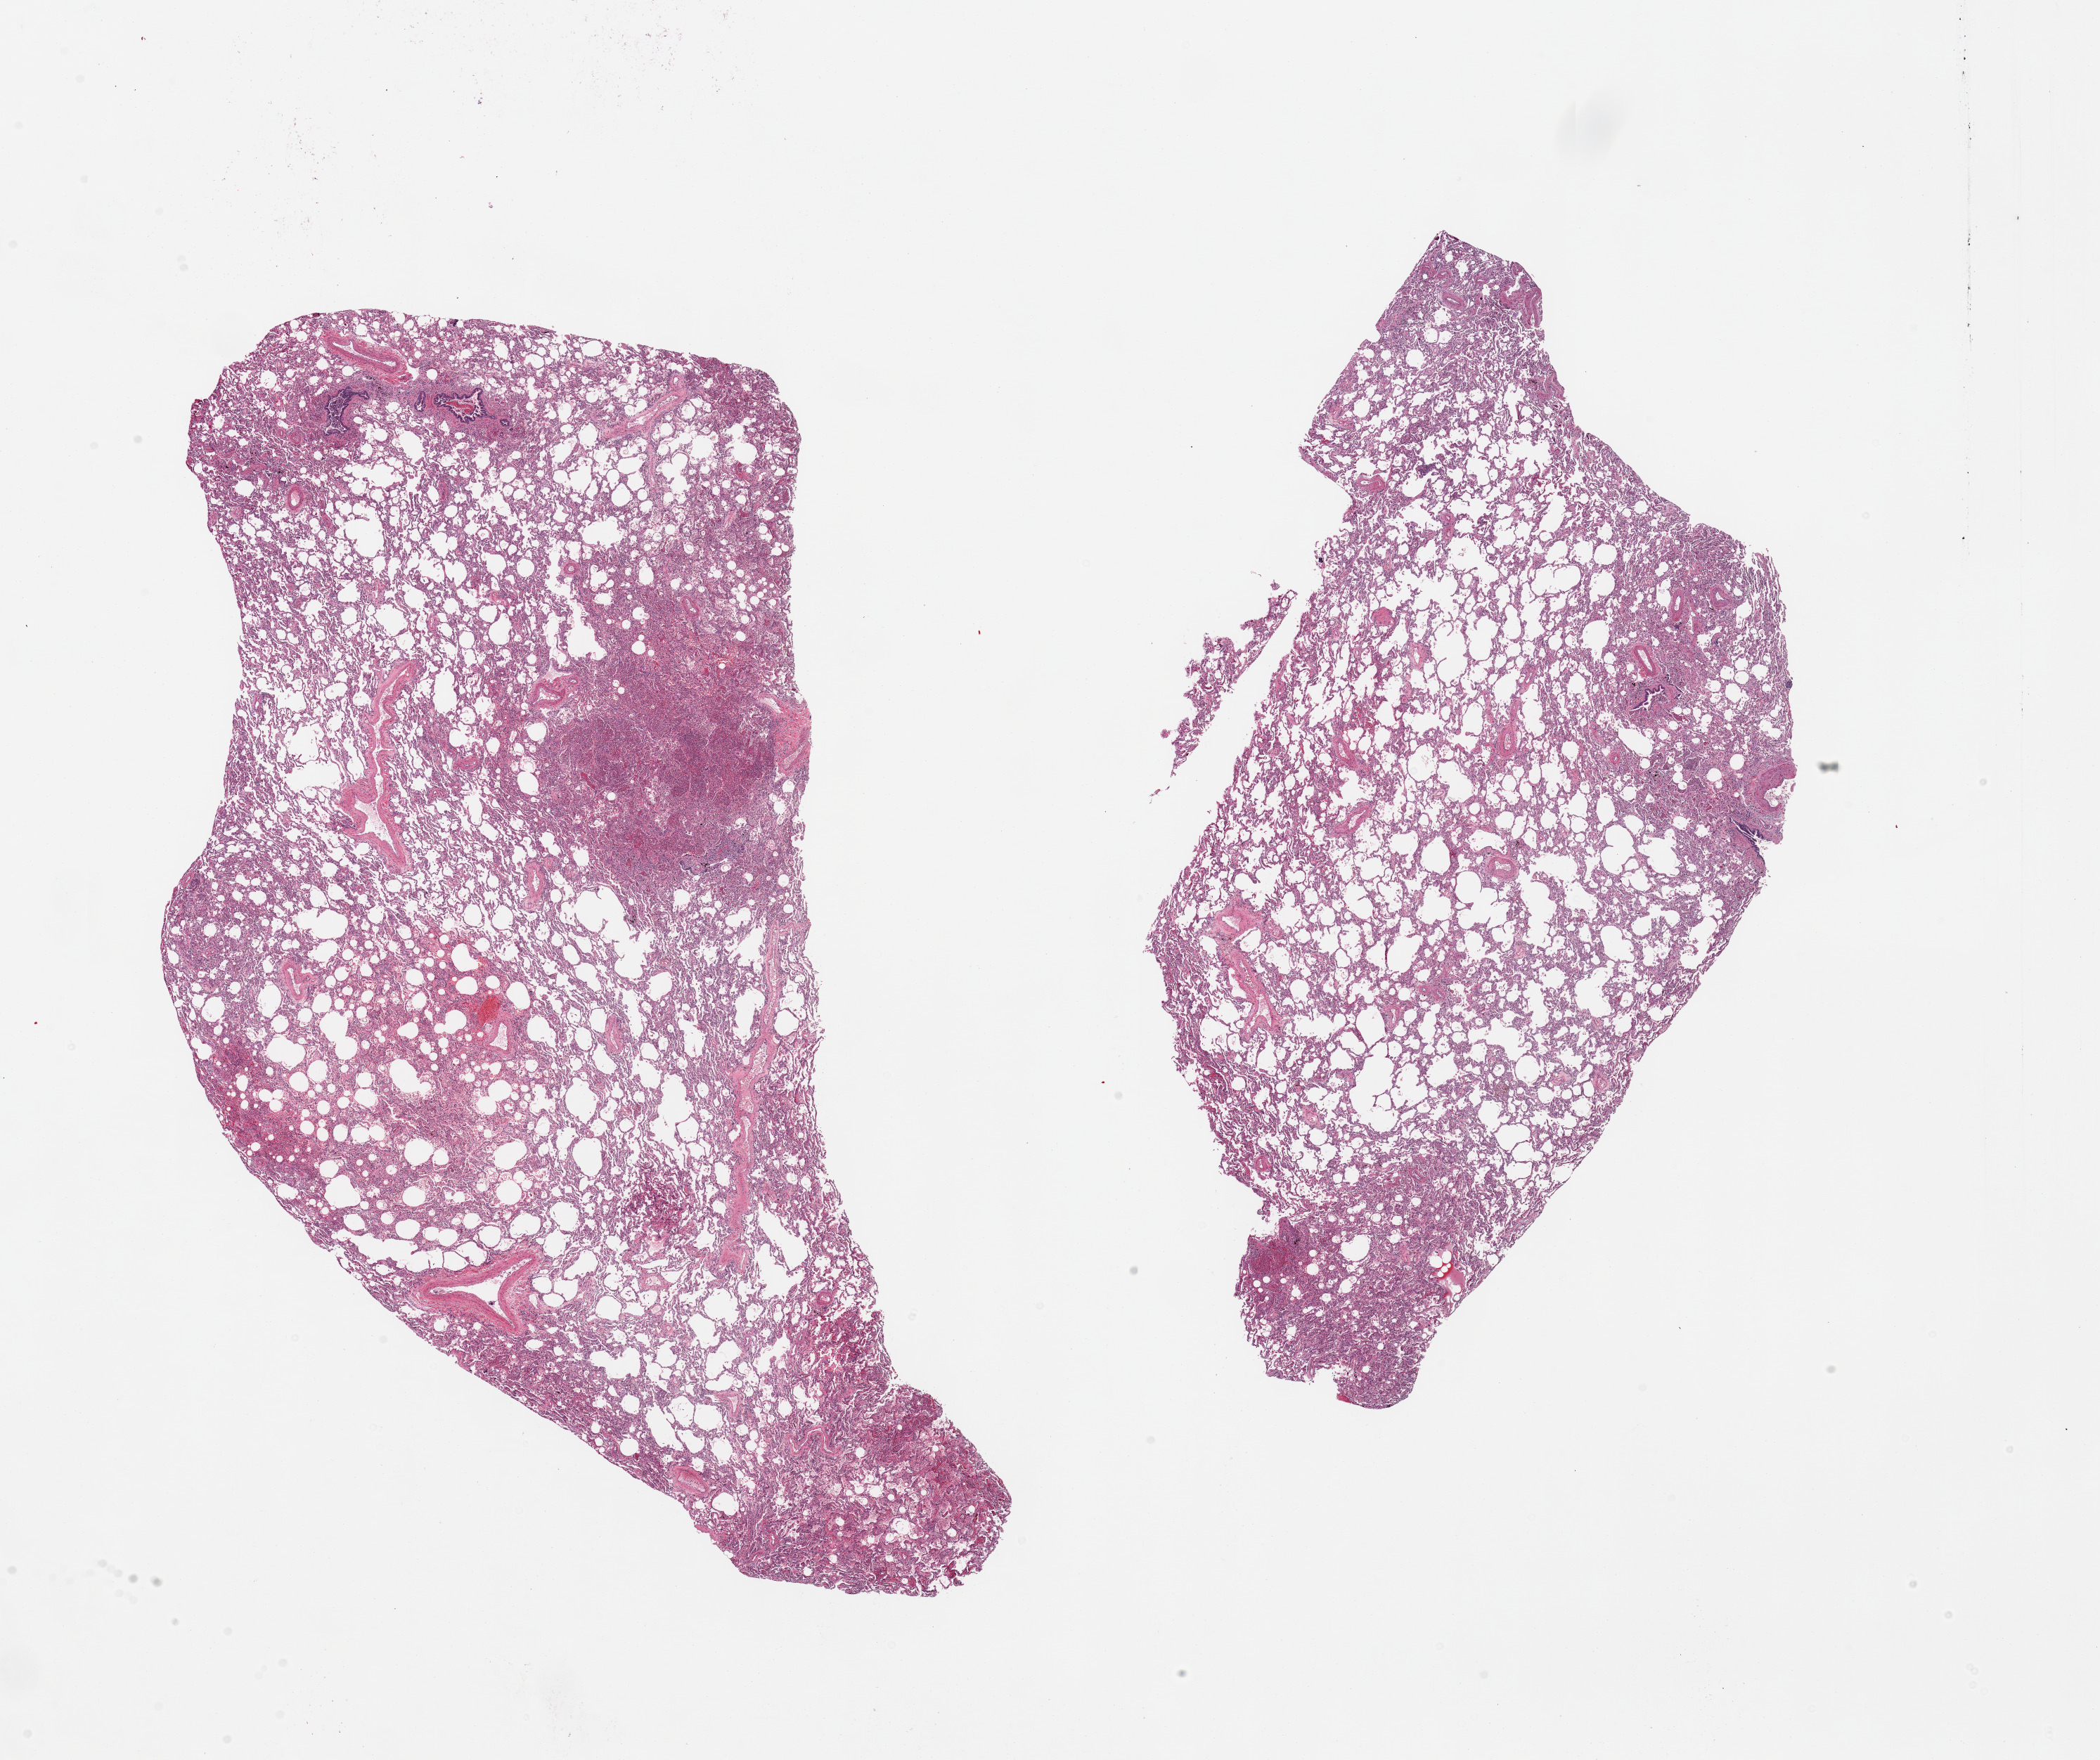
Digitized haematoxylin and eosin-stained section — shown as a low-resolution overview of the whole scanned area (about 23.6 x 19.8 mm). Donor: male.
Specimen: PAXgene-fixed, paraffin-embedded tissue; target tissue: lung; tissue donor sample.